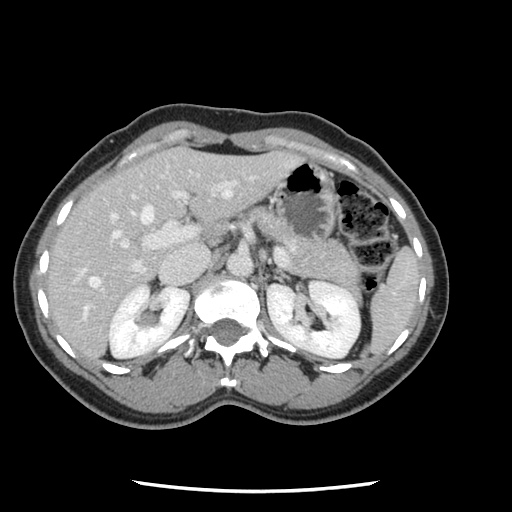
Contrast-enhanced abdominal CT, one axial slice; slice 73 of 134 in the series (ordered by position); 120 kVp; intravenous contrast given; soft-tissue window (W 400 / L 40 HU); 512 × 512 image matrix, field of view 330 × 330 mm. Female patient, age 43 years. Case-level facts recorded for this patient, not image findings: diagnosis: colorectal cancer liver metastases, imaged before liver resection; multiple liver metastases: yes; largest metastasis: 3.4 cm; disease in both lobes: yes.
Outlined on this slice (expert manual segmentation):
- hepatic veins: bounding box (x1, y1, x2, y2) in pixels: (84, 190, 231, 318)
- liver: (47, 148, 295, 359)
- planned liver remnant (the part of the liver to remain after resection): (47, 150, 186, 303)
- portal vein (with intrahepatic branches): (73, 181, 237, 283)